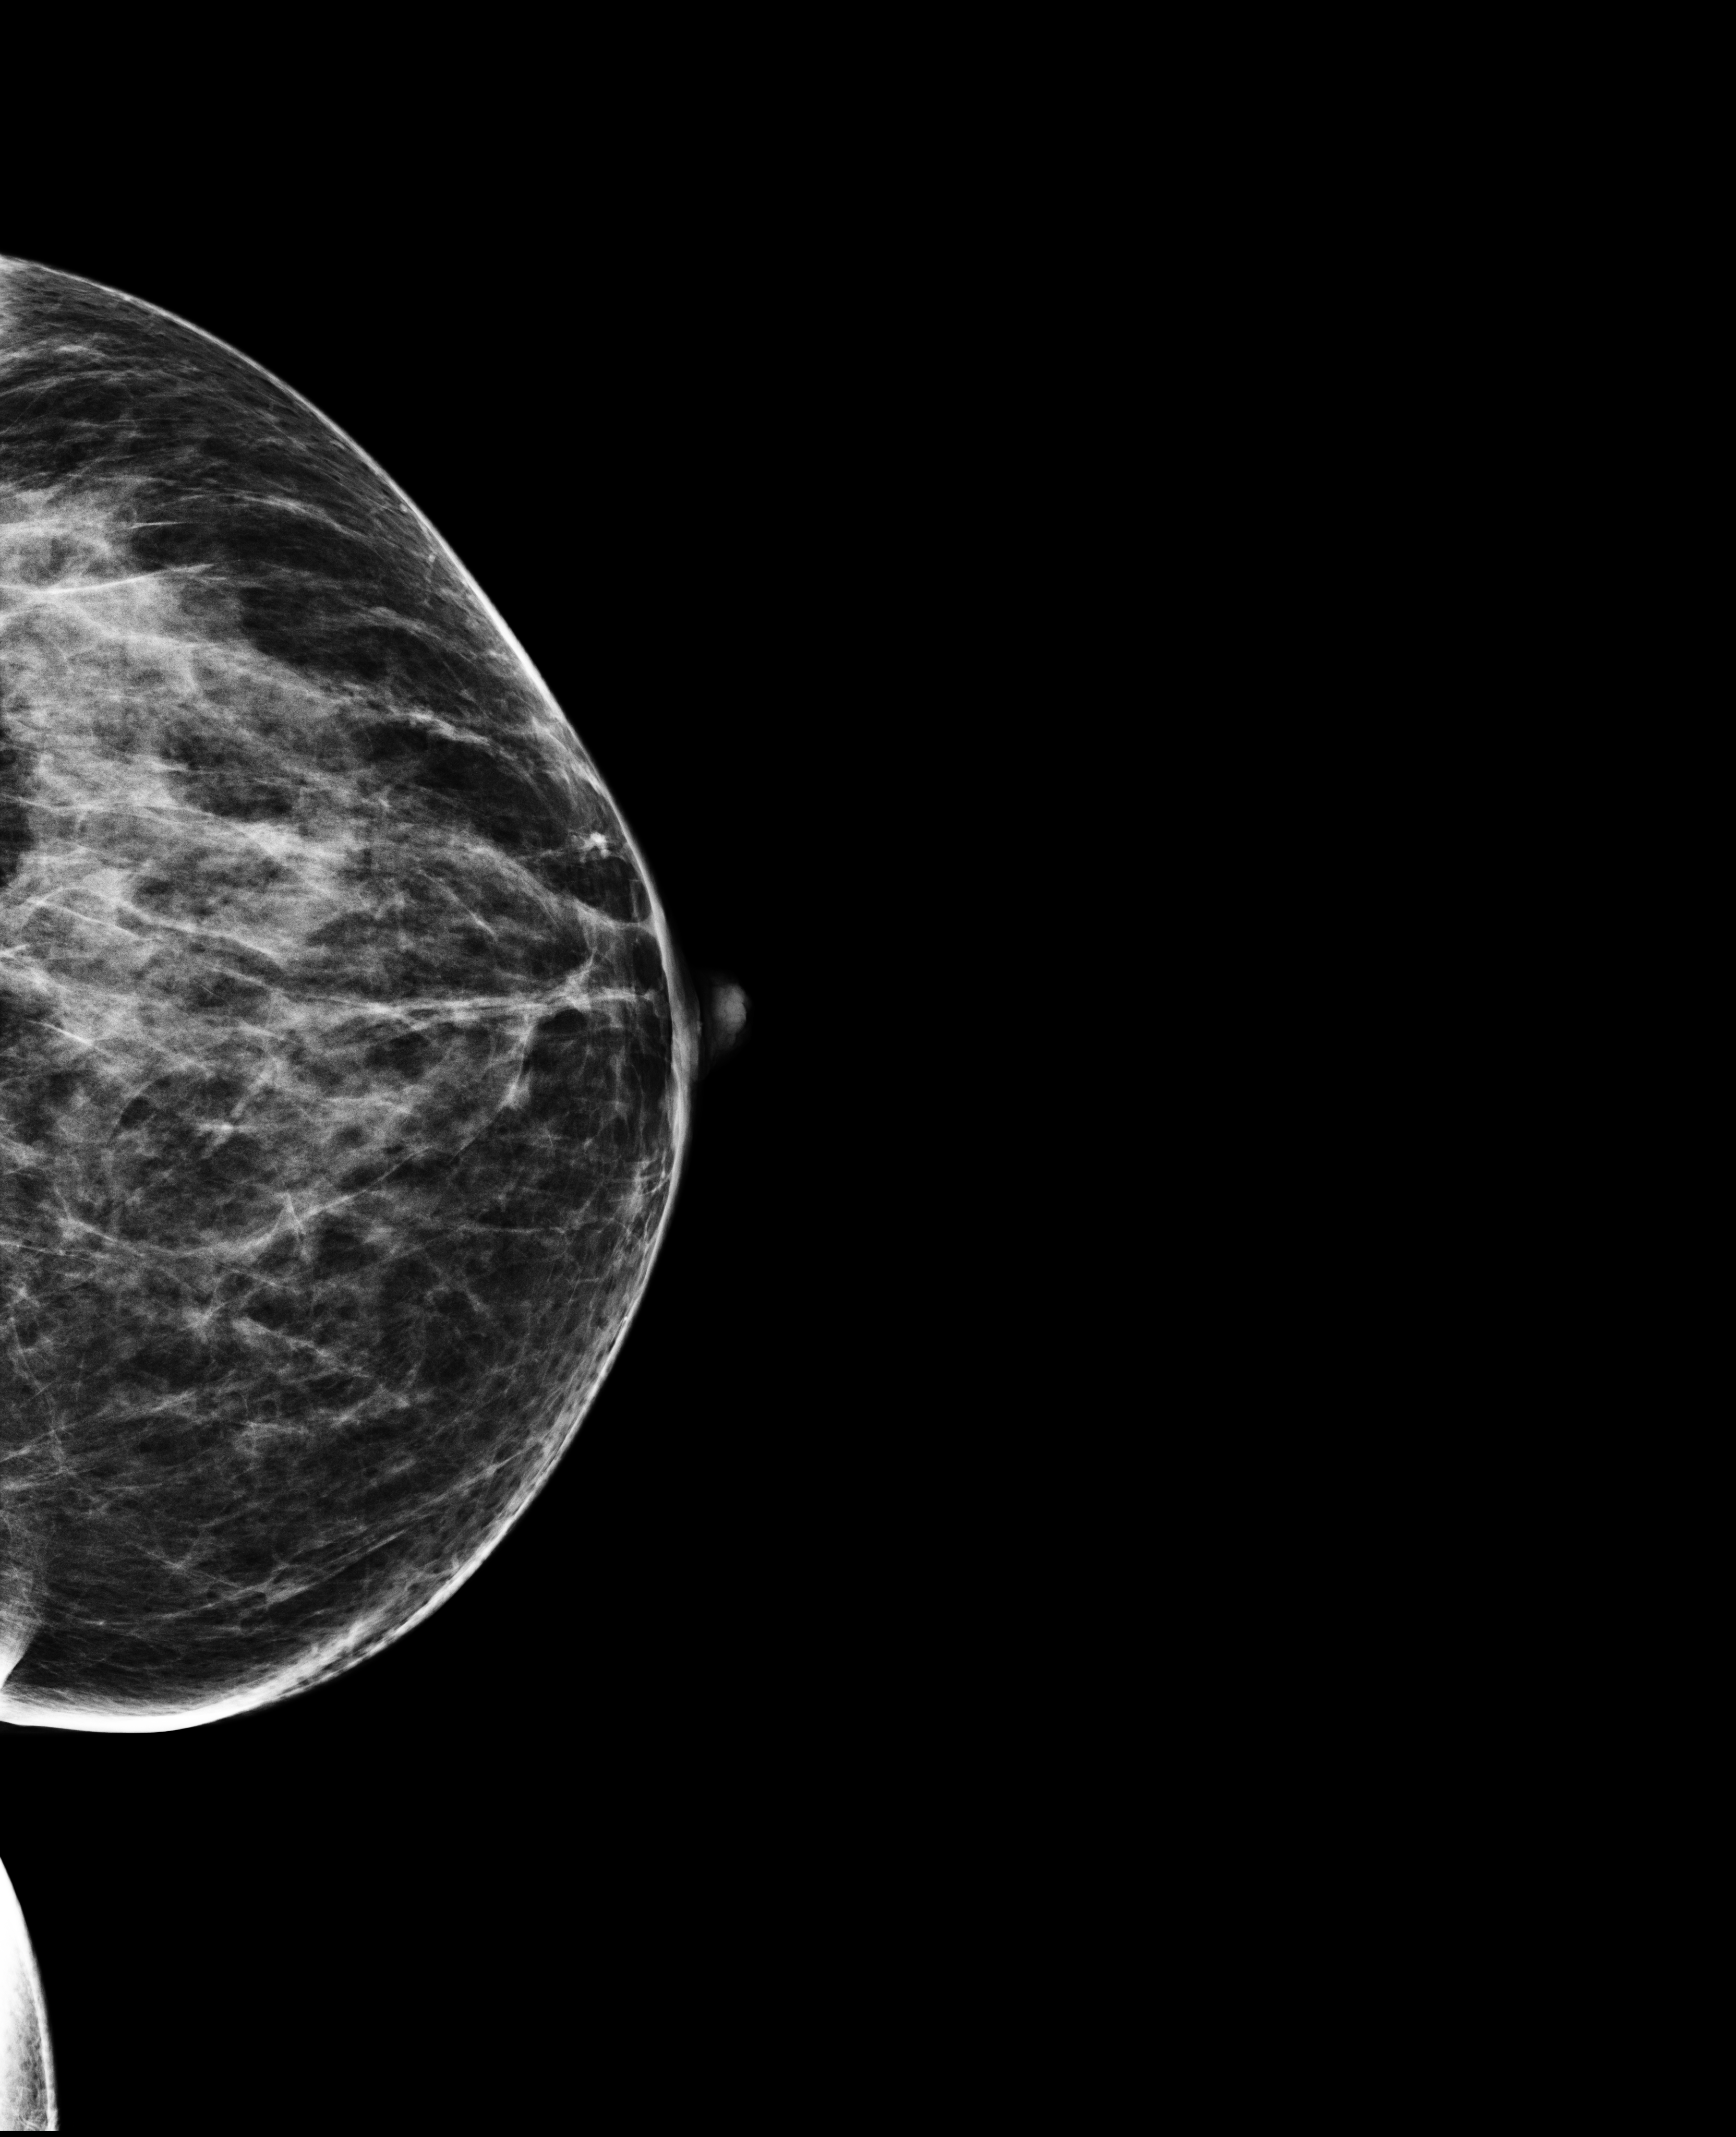
Digital mammogram (FFDM); left breast; craniocaudal (CC) view; annual screening mammography examination; compressed breast thickness 53 mm. Patient: female, 45 years.
Final BI-RADS category for the screening round (tomosynthesis exam, both breasts): category 1.